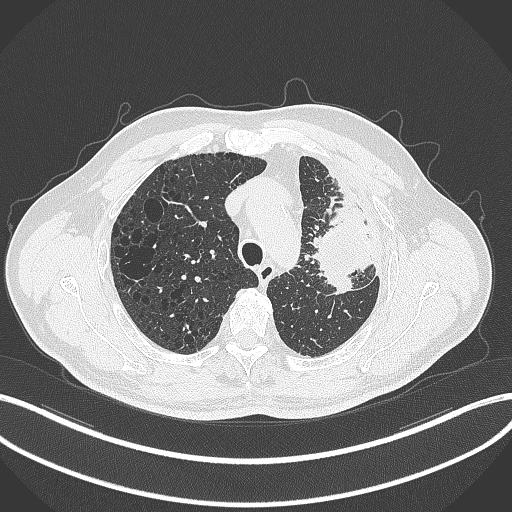
Chest CT, one axial slice. Position 245 of 297 along the scan axis. 120 kVp. Lung window (W 1500 / L -600 HU). 1 mm slice thickness. 512 × 512 image matrix, field of view 400 × 400 mm. Patient: male, 68 years. From the clinical record (not read from this slice): clinical TNM (as recorded): T3 N3 M1.
Annotated regions visible in this slice (rectangle marked by the reading radiologist):
- lung tumour (recorded histology: adenocarcinoma): bounding box <315,203,371,296> (left, top, right, bottom; pixels)